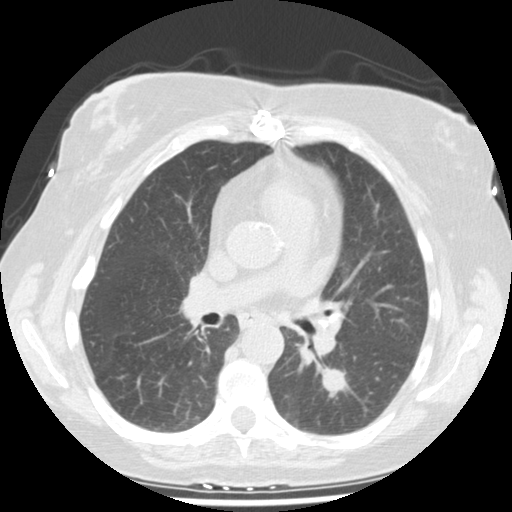
Chest CT (low-dose screening protocol), one axial image; second annual screen; lung window (W 1500 / L -600 HU); 2.5 mm slice thickness; 512 × 512 image matrix. Female, age 61 years at enrolment.
Expert-annotated lung lesion, bounding box <312,355,366,407> (left, top, right, bottom; pixels). The screening reader recorded 2 non-calcified nodules or masses ≥4 mm on this exam (left lower lobe, right upper lobe); which of them this box marks is not recorded. Official screen result: positive, change unspecified: nodule(s) >= 4 mm or enlarging nodule(s), mass(es), or other non-specific abnormalities suspicious for lung cancer. Lung cancer was diagnosed 69 days after this screen: squamous cell carcinoma, NOS, left lower lobe, moderately differentiated (G2), stage IA (AJCC 6th edition), 12 mm at pathology.